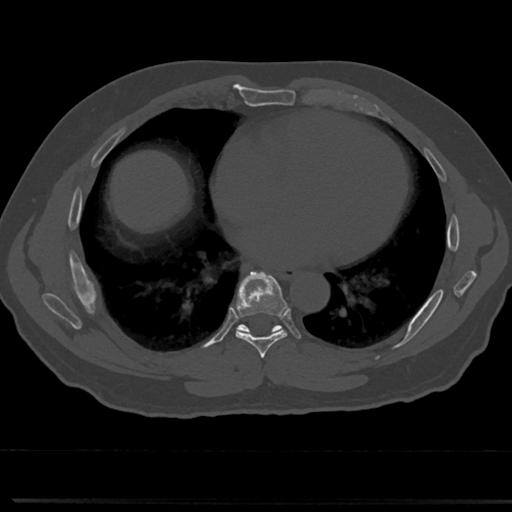
CT including the spine, one axial slice; position 391 of 817 along the scan axis; 120 kVp; bone window (W 1800 / L 400 HU); 0.5 mm slice thickness; 512 × 512 image matrix, field of view 355 × 355 mm. Male patient, age 61 years. Case-level facts recorded for this patient, not image findings: primary cancer: prostate.
Annotated regions visible in this slice (semi-automatically segmented with operator editing):
- T6 vertebra: bounding box [x1, y1, x2, y2] px = [260, 358, 269, 377]
- T7 vertebra: [214, 275, 310, 357]